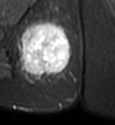
MRI of an extremity soft-tissue mass, one axial slice; slice 22 of 49 in the series (ordered by position); STIR; MR volume resampled by the dataset authors to the PET/CT grid (not the native acquisition matrix); 115 × 125 image matrix, field of view 112 × 122 mm. Female patient. From the clinical record (not read from this slice): histological type: epithelioid sarcoma; grade: intermediate; site of the primary tumour: right buttock.
Annotated regions visible in this slice (expert contour drawn on MRI and transferred to this co-registered scan by the dataset authors):
- gross tumour volume including surrounding oedema: box from (x=17, y=18) to (x=71, y=79) px
- gross tumour volume (mass): (x=20, y=23)–(x=71, y=76)